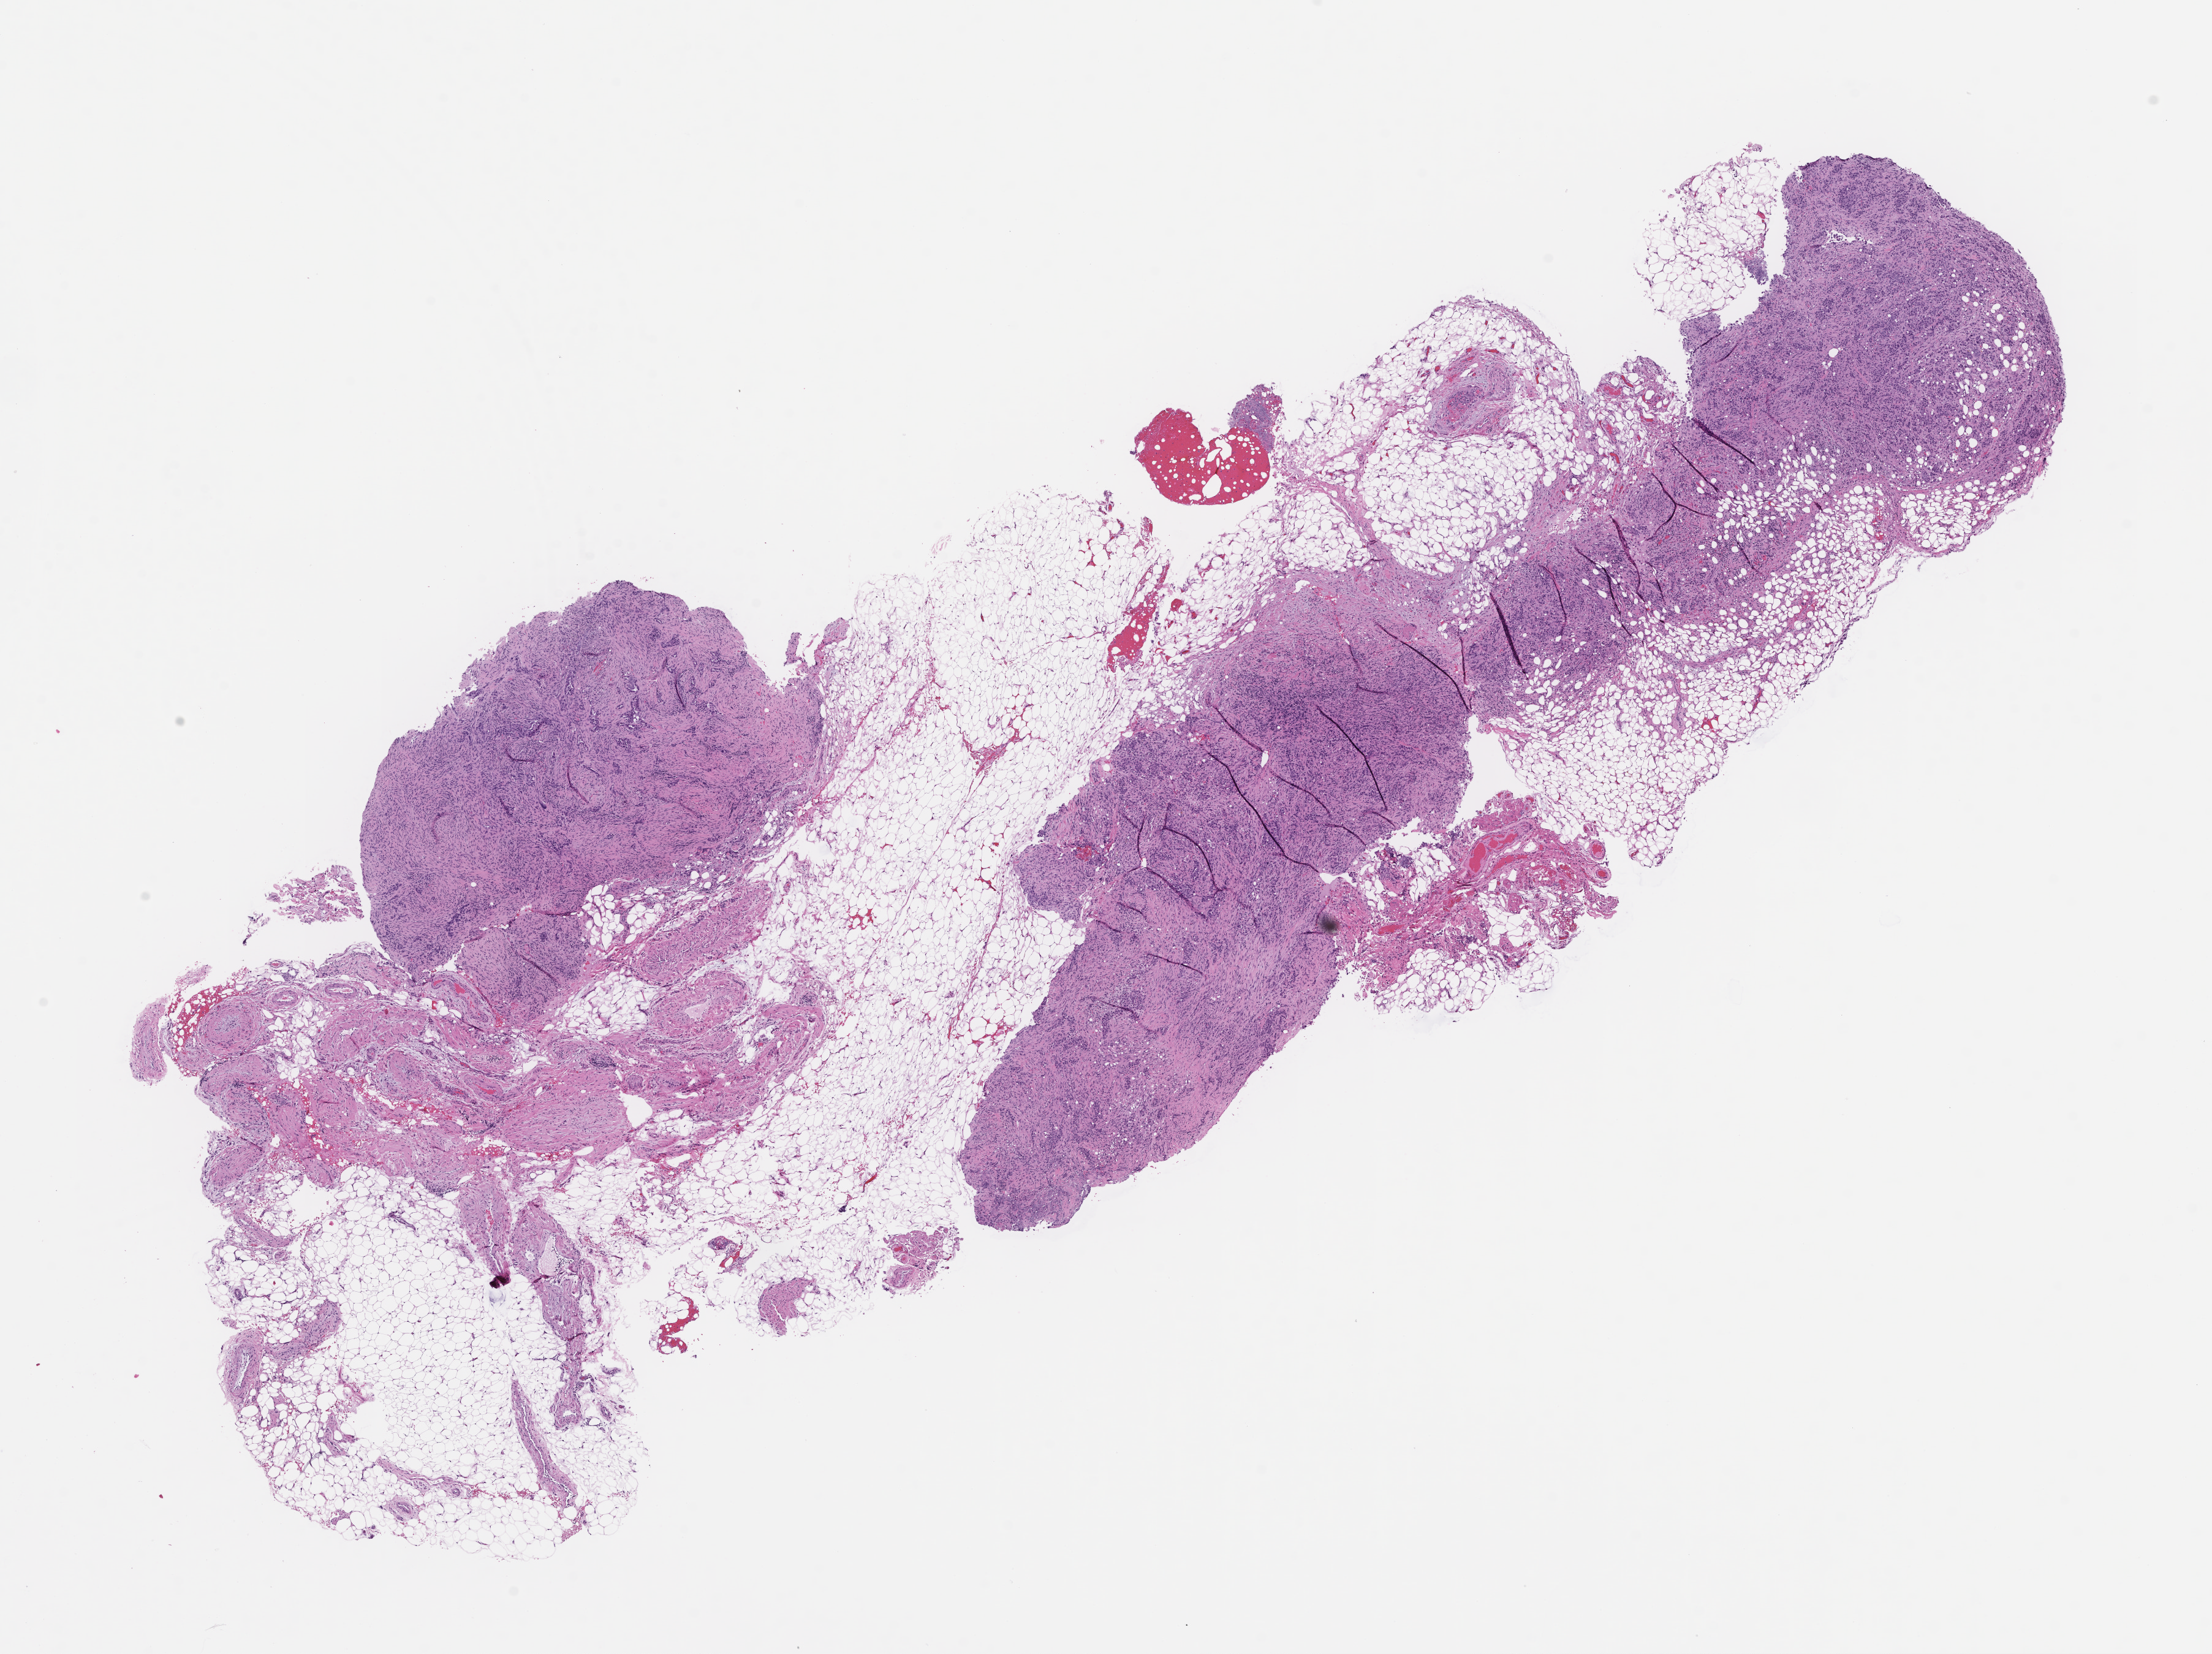
Haematoxylin and eosin whole-slide image — shown as a low-resolution overview of the whole scanned area (about 14.6 x 10.9 mm), formalin-fixed, paraffin-embedded (FFPE) tissue. Patient: female.
This section: metastasis (sampled organ not recorded). Patient diagnosis (primary): Non-Small Cell Lung Carcinoma.